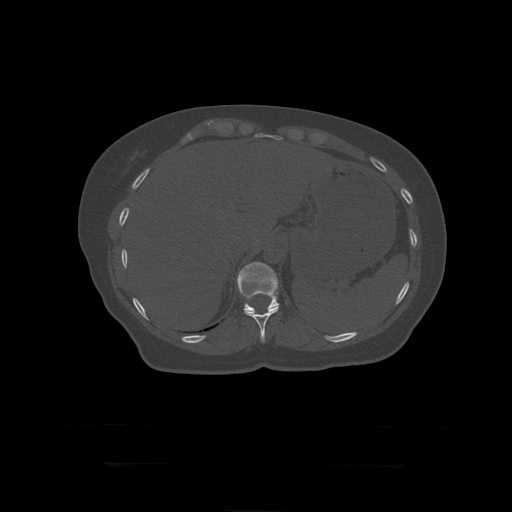
CT including the spine, one axial slice; position 211 of 399 along the scan axis; reconstruction kernel STANDARD; bone window (W 1800 / L 400 HU); 1.25 mm slice thickness; 512 × 512 image matrix. Patient age 41 years. Case-level facts recorded for this patient, not image findings: primary cancer: breast.
Outlined on this slice (semi-automatic segmentation, software-assisted and operator-edited):
- T11 vertebra: bounding box [x1, y1, x2, y2] px = [244, 305, 280, 342]
- T12 vertebra: [237, 262, 280, 312]